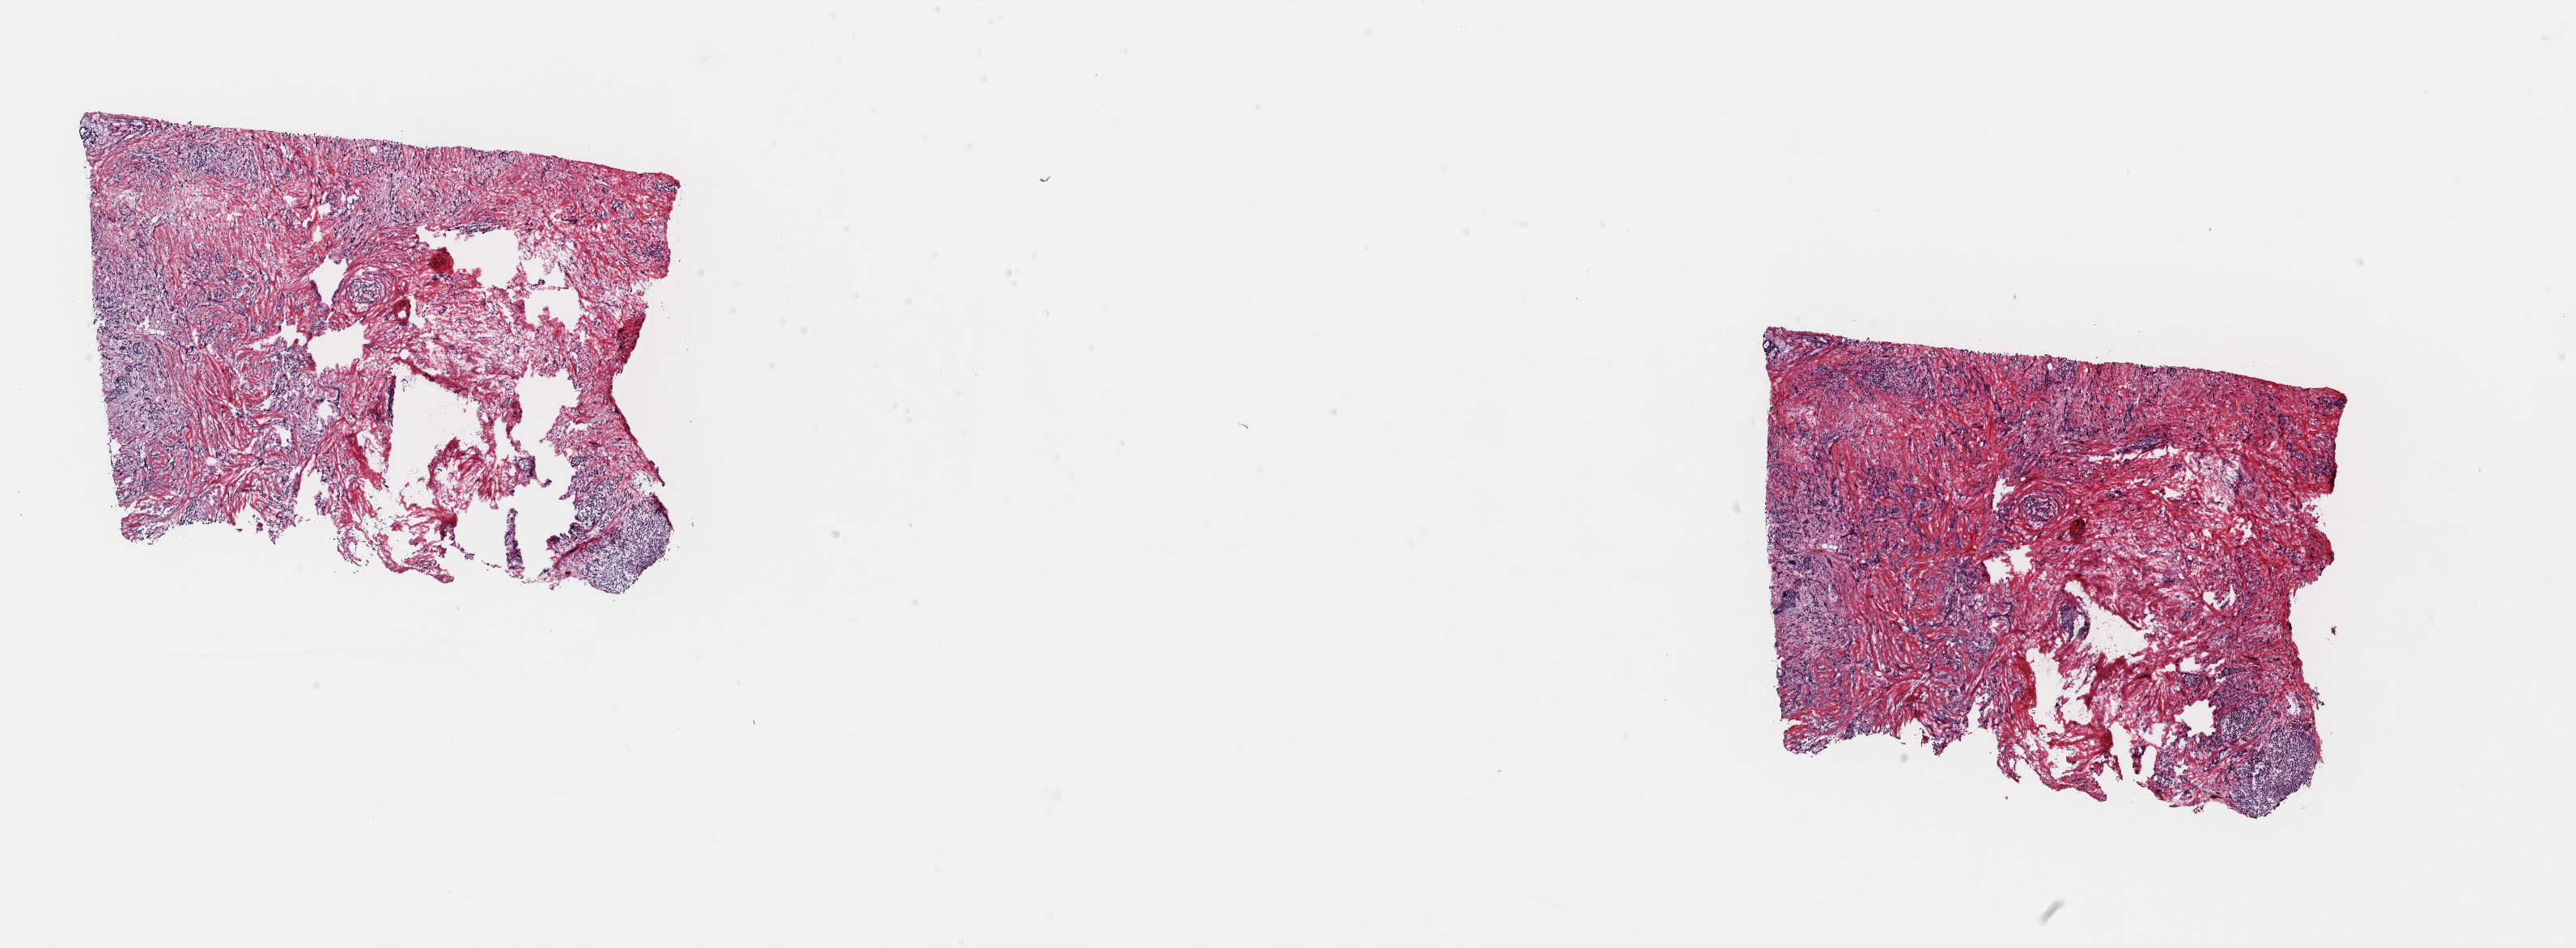
Whole-slide histology image, H&E — shown as a low-resolution overview of the whole scanned area (about 25.1 x 9.3 mm, from a 40x scan); frozen section from the top of the tissue portion; sample: primary tumour, breast. Female, age 56 years at initial diagnosis. Composition of this section per pathologist review: tumour cells 100%, tumour nuclei 75%, normal cells 0%, stromal cells 0%, necrosis 0%. Inflammatory infiltration, as recorded: lymphocyte infiltration 2%, monocyte infiltration 1%, neutrophil infiltration 0%.
• TNM: T3 N3a M0
• AJCC pathologic stage: IIIC (7th edition)
• lymph nodes positive (case pathology): 19 of 22 examined
• pathologic diagnosis: Lobular carcinoma, NOS
• laterality: left